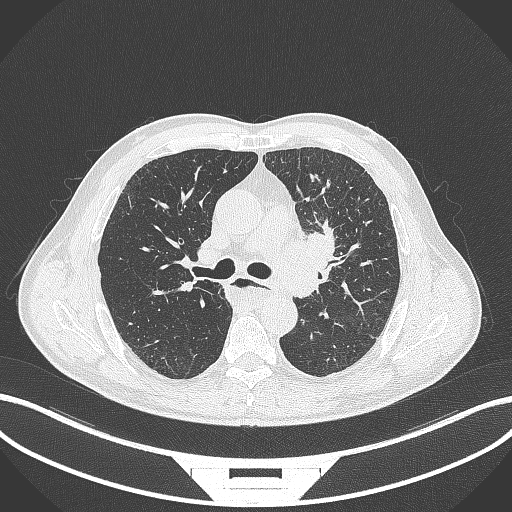
Chest CT, one axial slice; position 238 of 411 along the scan axis; reconstruction kernel B70f; 120 kVp; lung window (W 1500 / L -600 HU); 1 mm slice thickness; 512 × 512 image matrix. Patient: male, 57 years. Case-level facts recorded for this patient, not image findings: clinical TNM (as recorded): T2a N1 M0.
Outlined on this slice (rectangle marked by the reading radiologist):
- lung tumour (recorded histology: squamous cell carcinoma): bounding box [x1, y1, x2, y2] px = [271, 219, 346, 300]